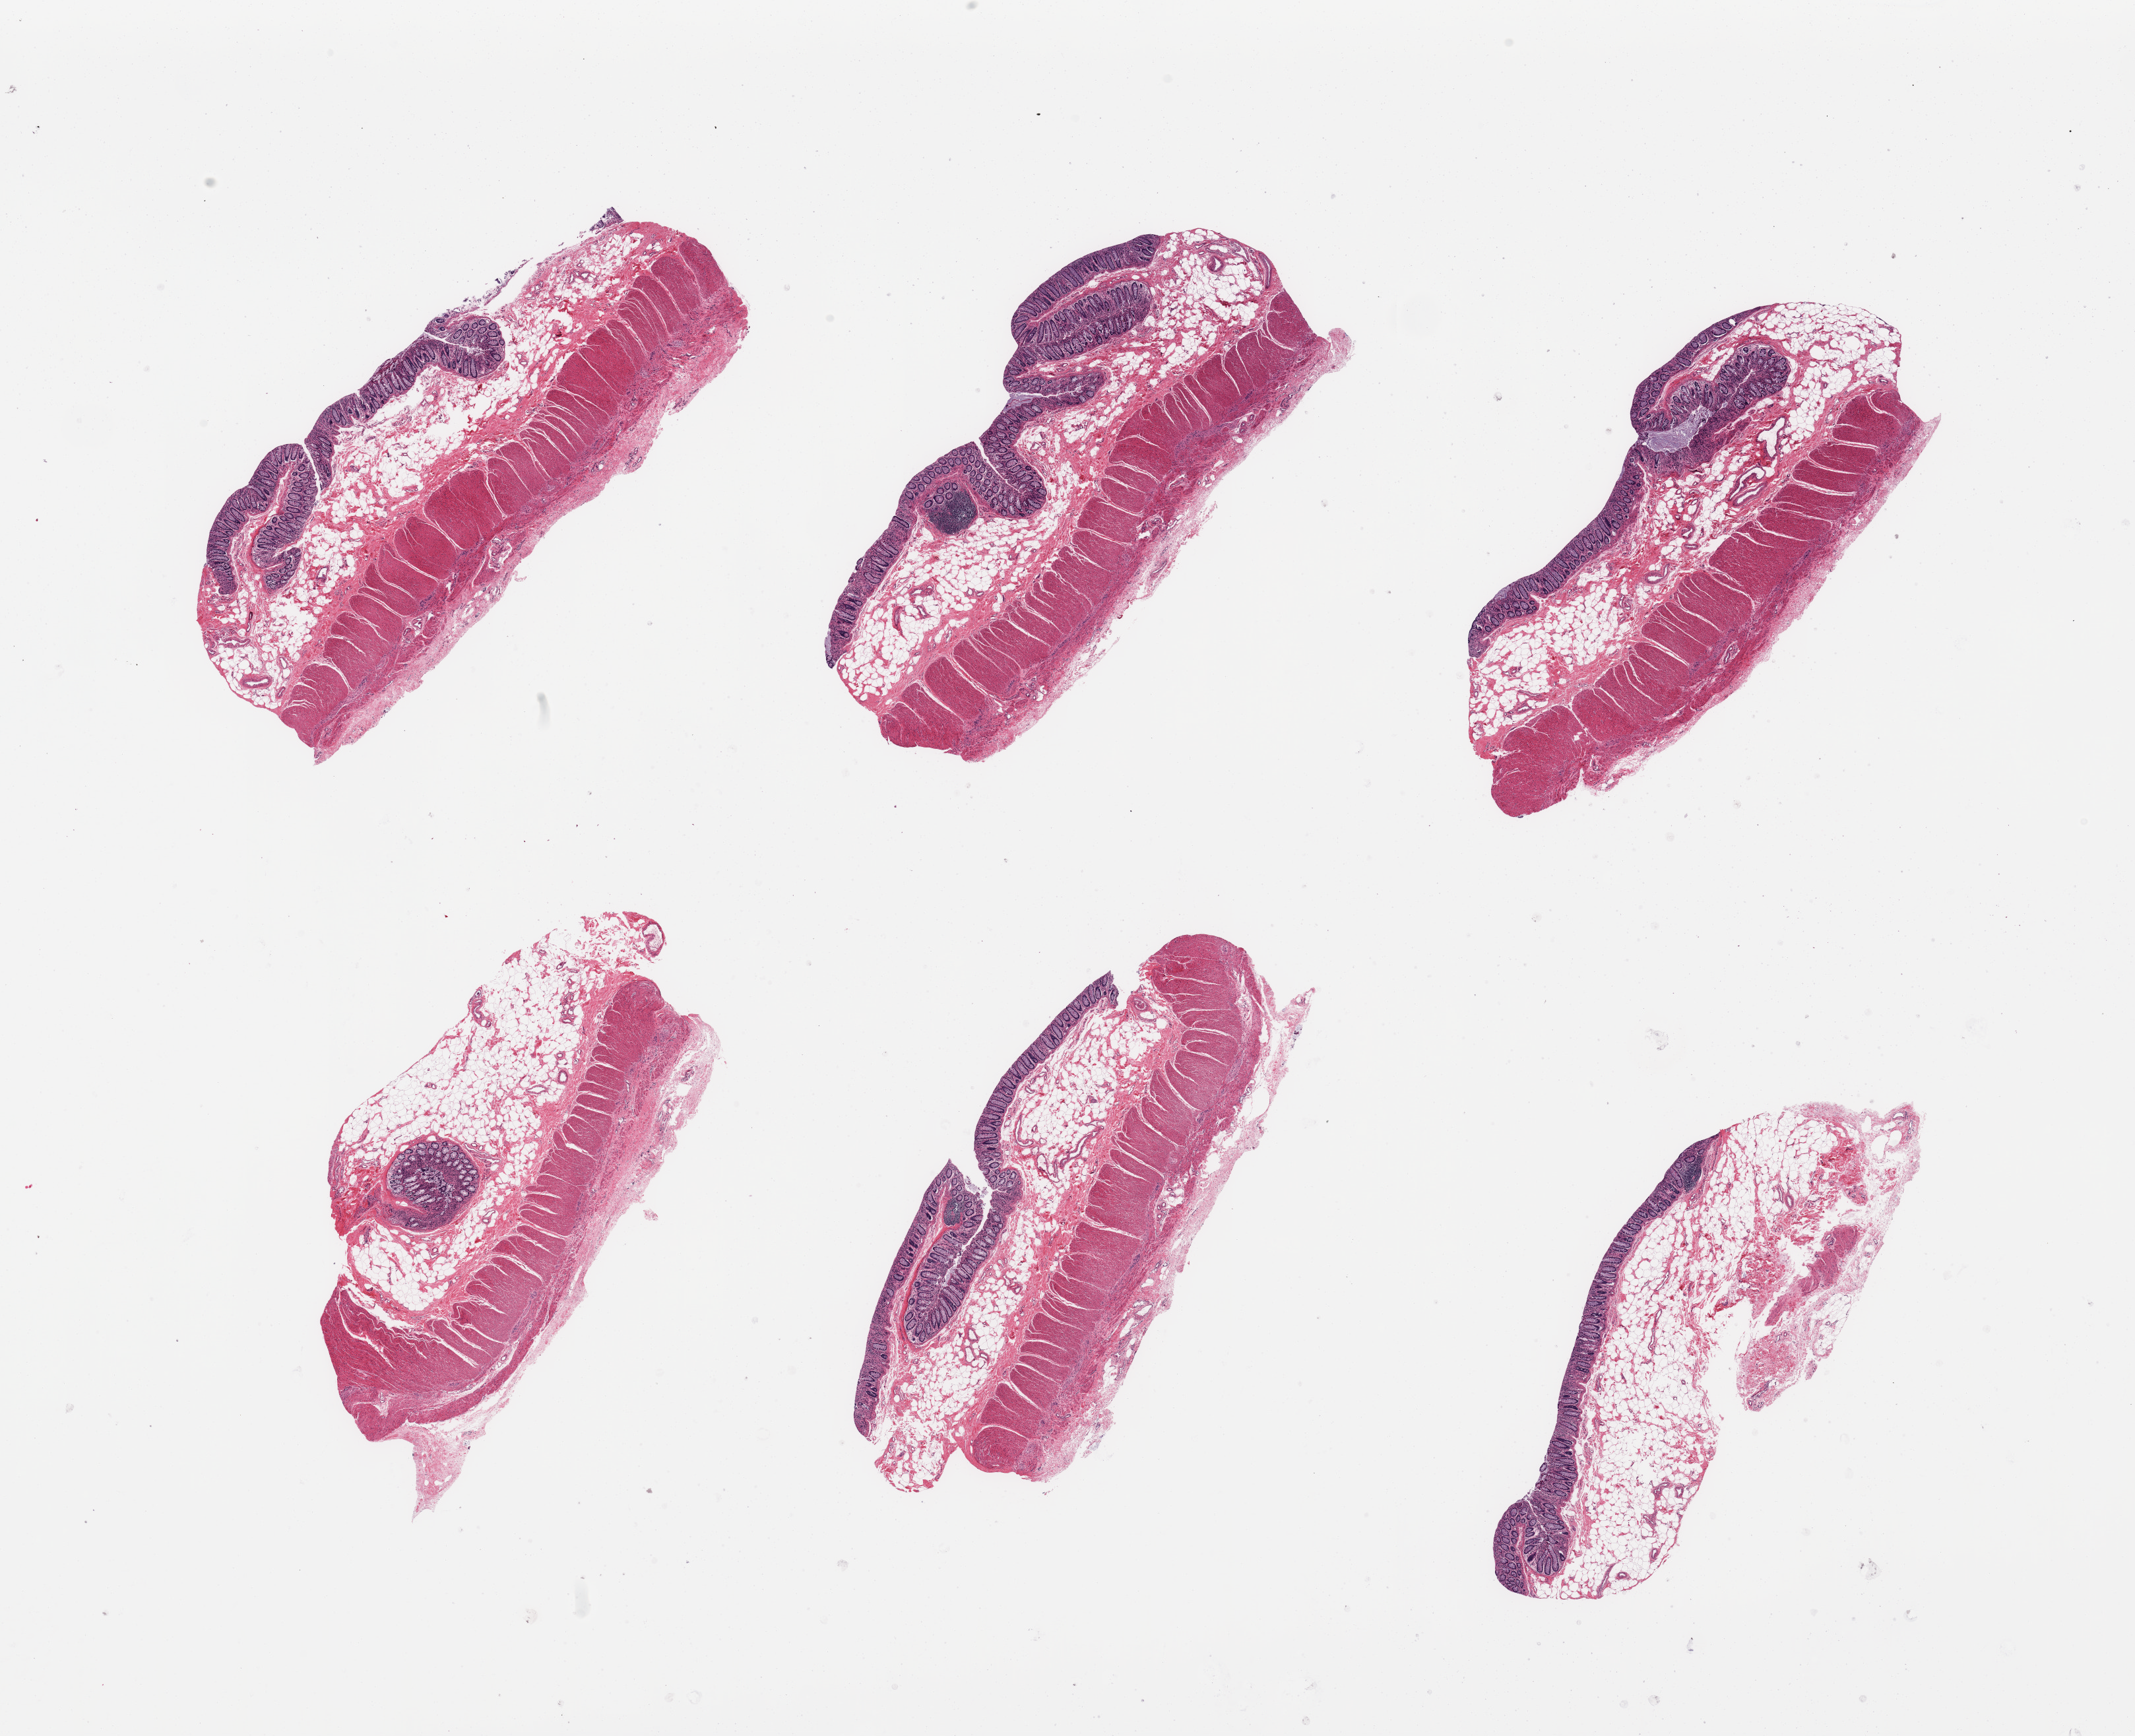
Digitized hematoxylin and eosin (H&E)-stained section, a low-resolution overview of the entire scanned area, about 25.6 x 20.8 mm (from a 20x scan), PAXgene-fixed, paraffin-embedded tissue, section of transverse colon (target tissue), tissue donor sample. Donor: male.
Reviewer comment on this tissue sample: 6 pieces; very focal severe mucosal autolysis; preserved muscularis.